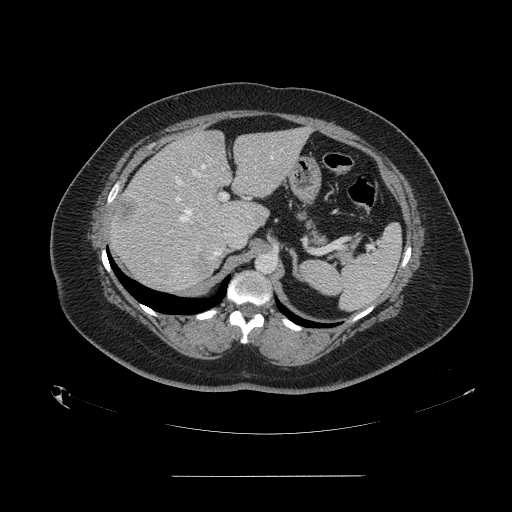
Contrast-enhanced abdominal CT, one axial slice. Slice 101 of 164 in the series (ordered by position). 120 kVp. Intravenous contrast given. Soft-tissue window (W 400 / L 40 HU). 2.5 mm slice thickness. 512 × 512 image matrix. Female patient, age 52 years. From the clinical record (not read from this slice): diagnosis: colorectal cancer liver metastases, imaged before liver resection; multiple liver metastases: yes; largest metastasis: 3.5 cm.
Structures marked on this image (expert manual segmentation):
- hepatic veins: bounding box <179,157,273,222> (left, top, right, bottom; pixels)
- liver: <111,129,308,292>
- planned liver remnant (the part of the liver to remain after resection): <174,129,308,229>
- portal vein (with intrahepatic branches): <174,176,228,202>
- liver metastasis: <193,254,209,272>
- liver metastasis: <250,212,263,224>
- liver metastasis: <119,199,137,223>